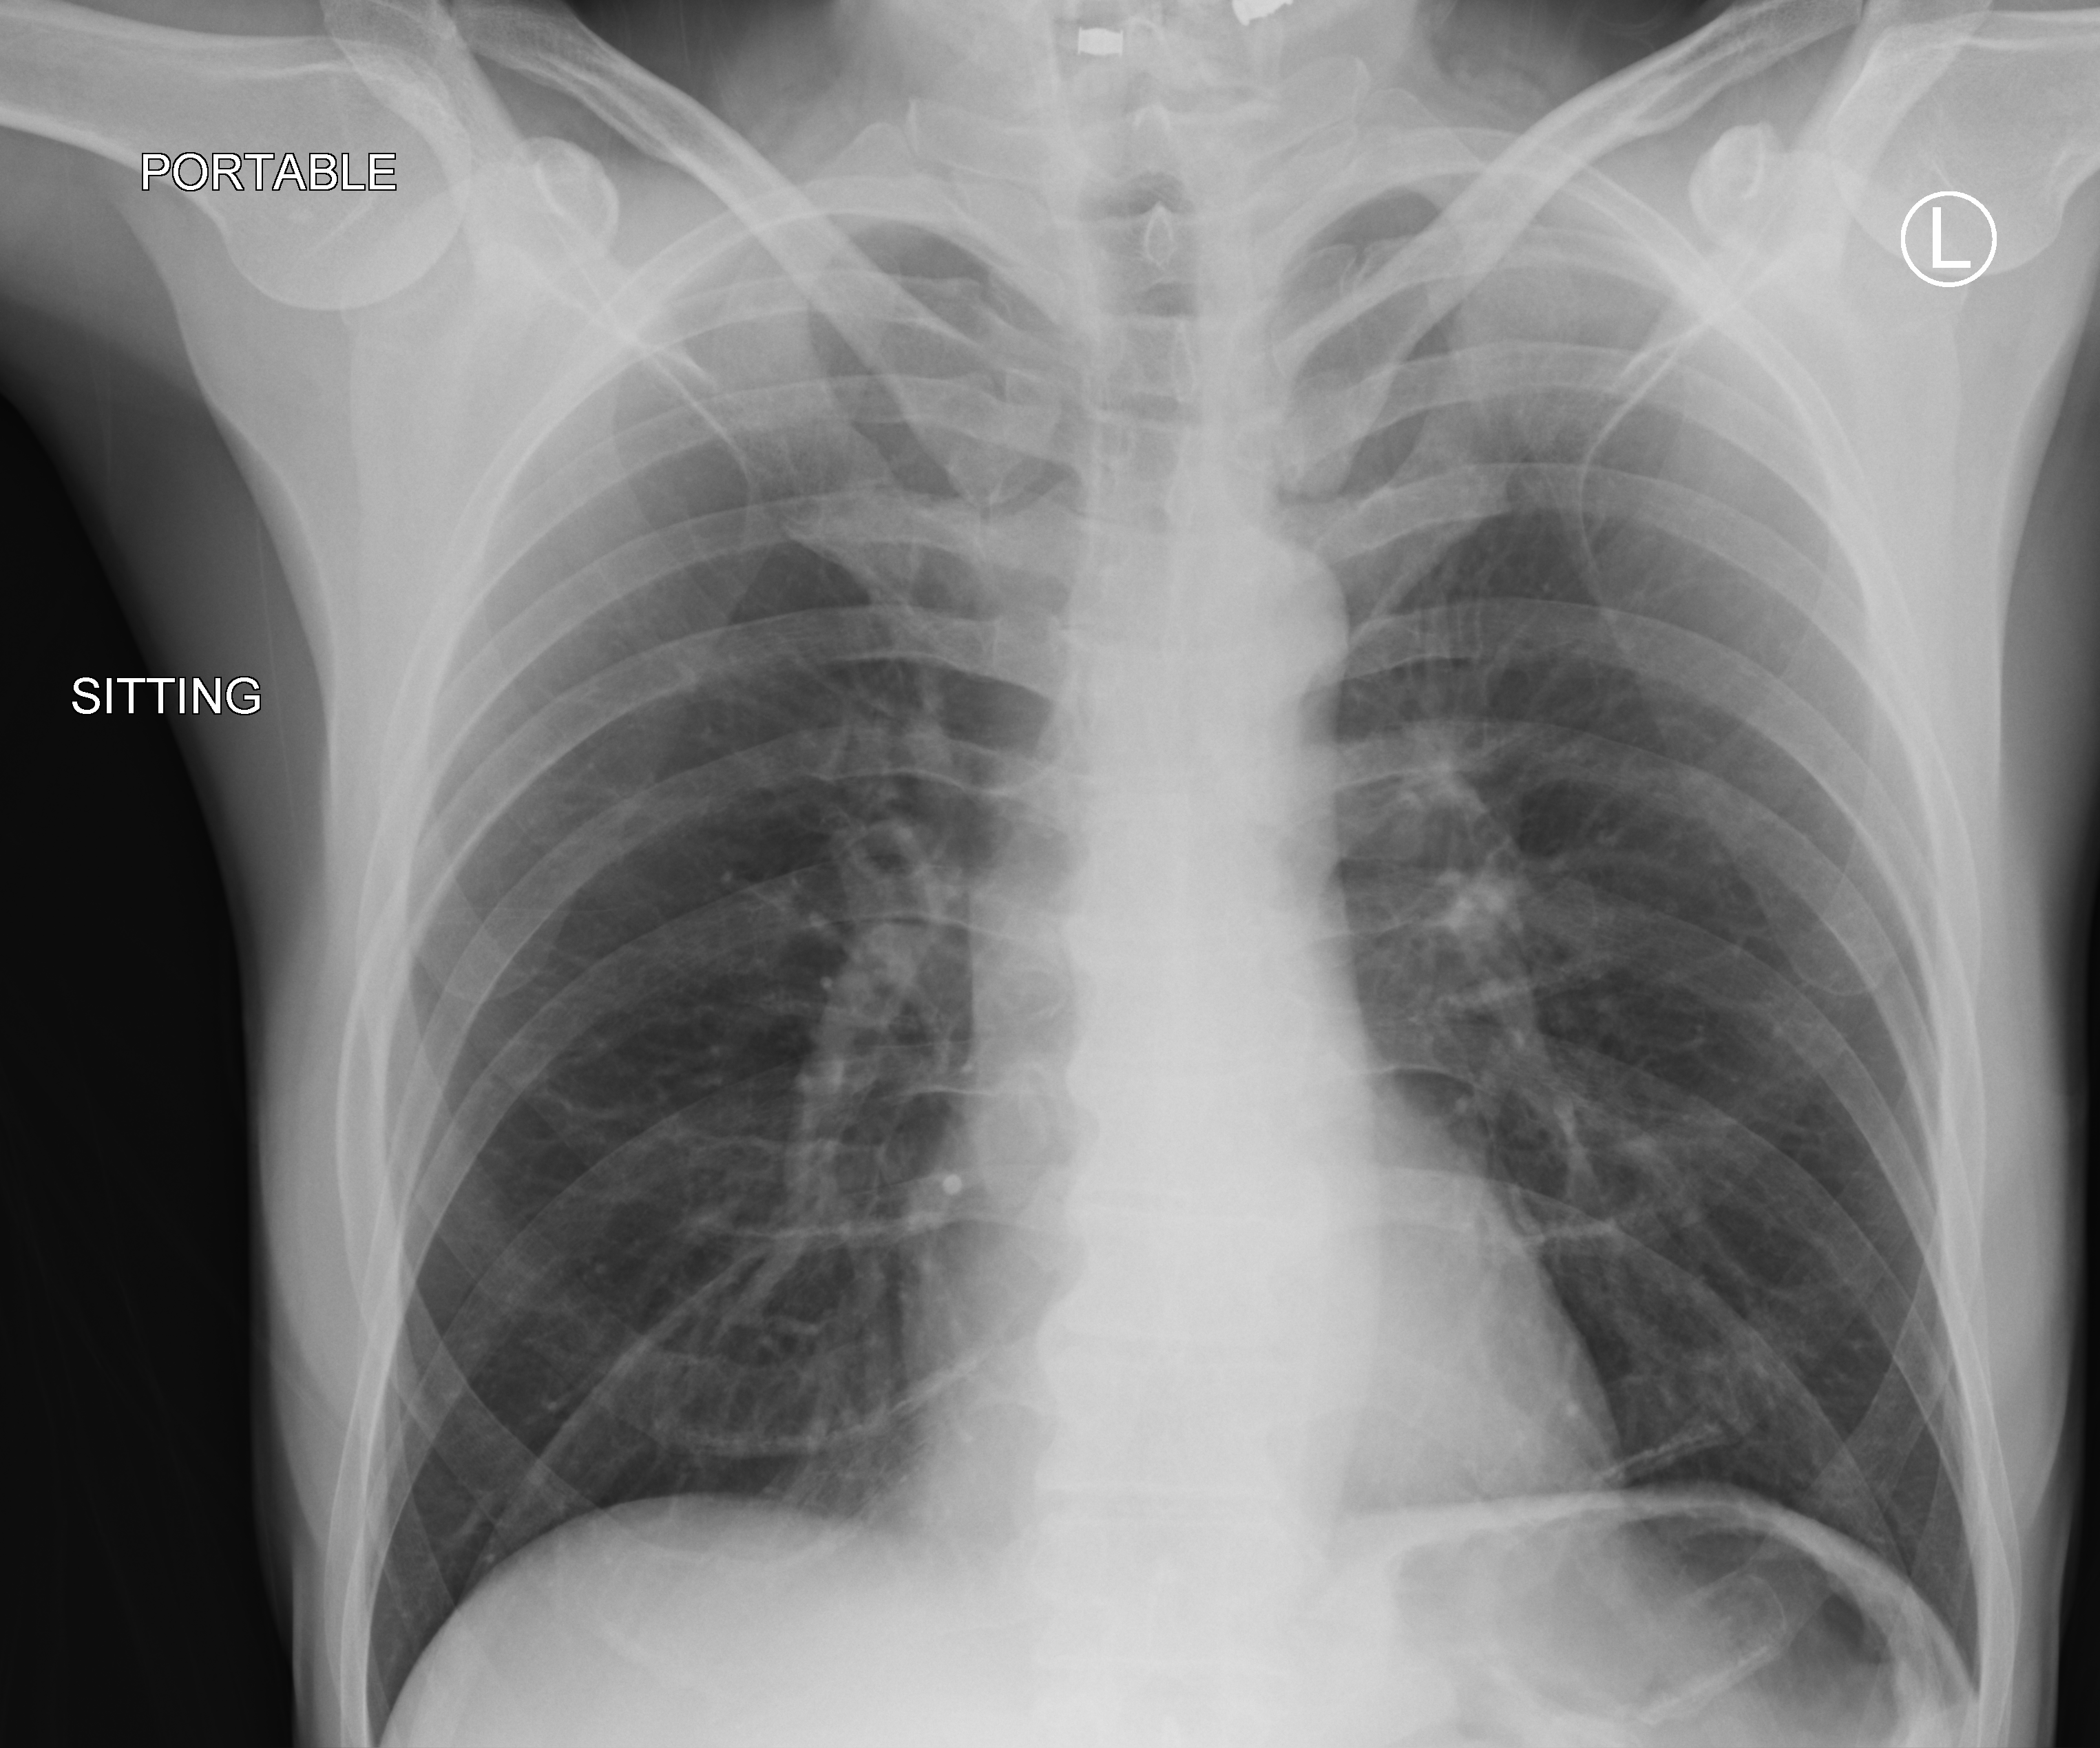
Portable chest radiograph; anteroposterior (AP) projection. Male patient hospitalised with COVID-19, age 18–59 years.
Hospital-stay facts (about this admission, not read from this image; timing relative to this image not recorded): diabetes (admission record): no; mechanically ventilated during this hospital stay: no.